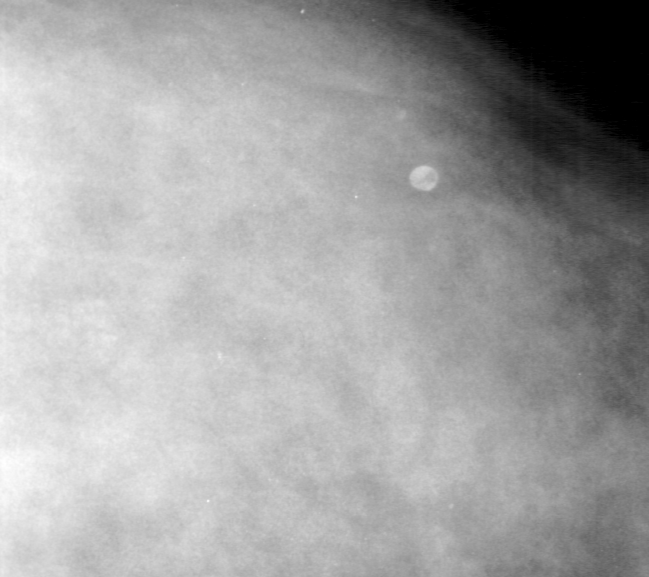
Cropped region of a digitized screen-film mammogram centred on a radiologist-marked abnormality; right breast; CC view.
- Marked abnormality: calcifications, morphology punctate, distribution segmental; BI-RADS assessment category 4; pathology result (as recorded, not read from the image): benign.